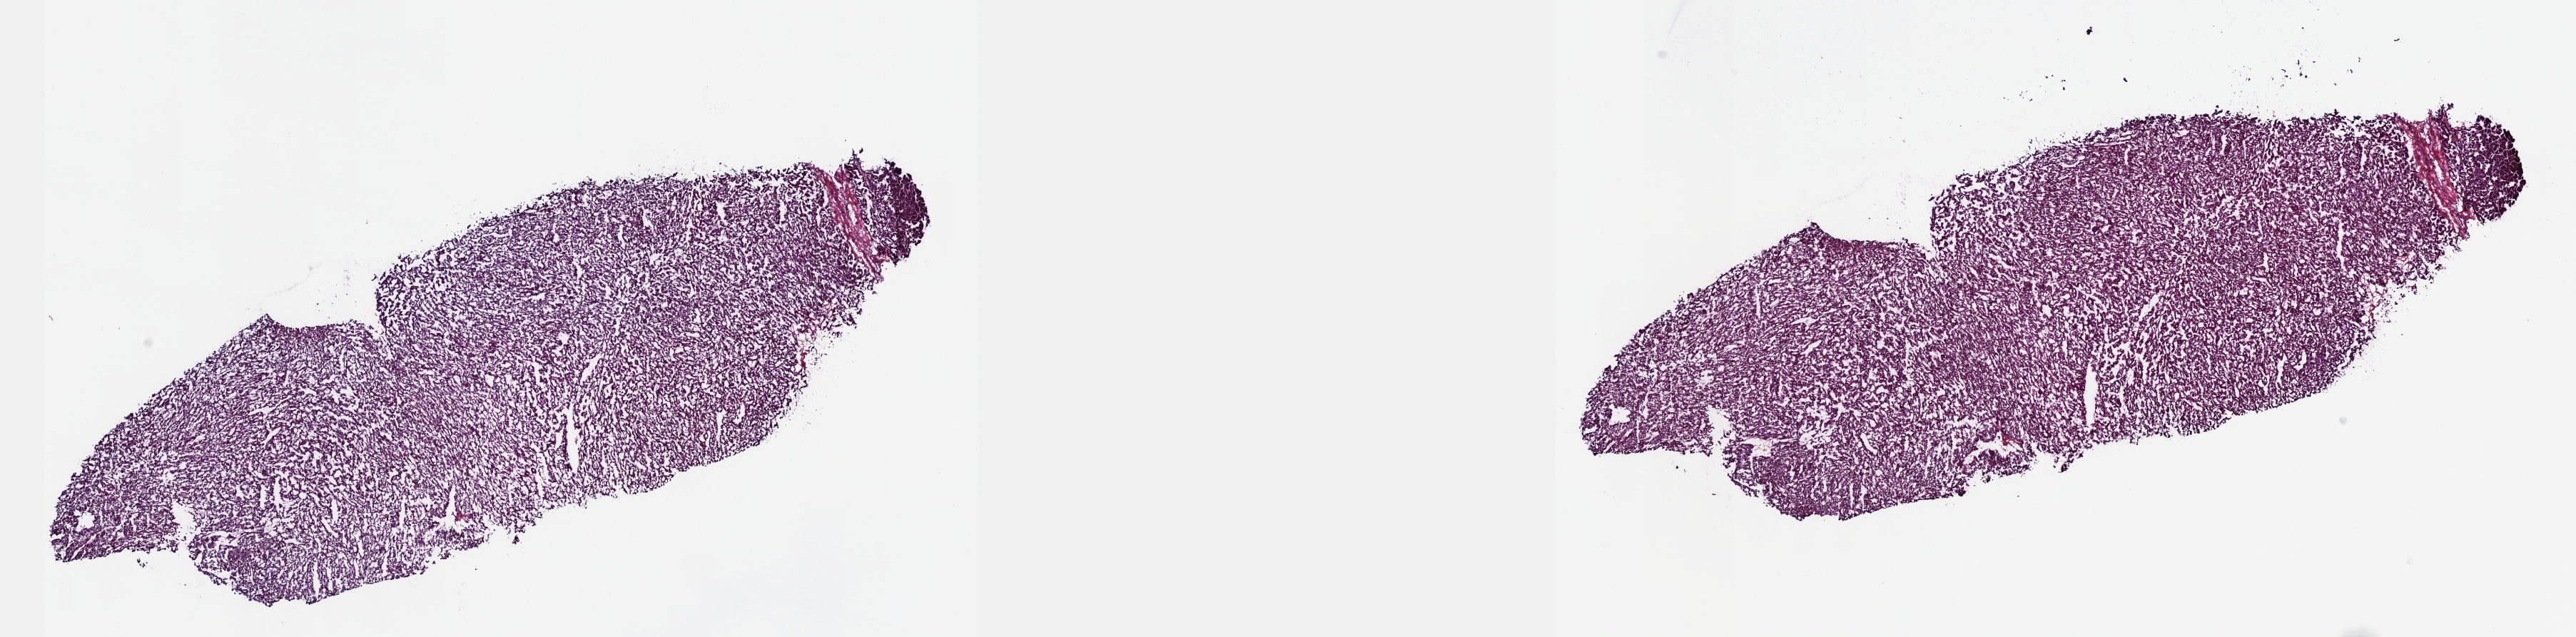
Whole-slide histology image, H&E-stained, shown as a low-resolution overview of the whole scanned area (about 29.2 x 7.2 mm), frozen section, liver, primary tumour sample. Patient: female, age at initial diagnosis 33 years. Pathologist review of this section (percent, as recorded): tumour cells 95%, tumour nuclei 95%.
Diagnosis: Hepatocellular carcinoma, NOS.